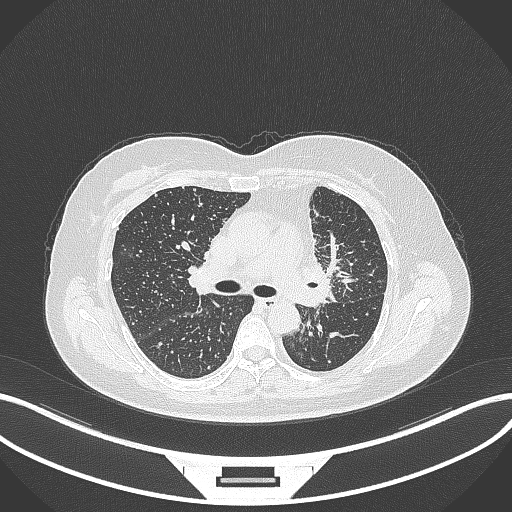
Chest CT, one axial slice; position 207 of 348 along the scan axis; reconstruction kernel B70f; 120 kVp; lung window (W 1500 / L -600 HU); 512 × 512 image matrix, field of view 400 × 400 mm. Female patient, age 49 years. Case-level facts recorded for this patient, not image findings: clinical TNM (as recorded): T1c N0 M1.
Outlined on this slice (rectangle marked by the reading radiologist):
- lung tumour (recorded histology: adenocarcinoma): box from (x=290, y=250) to (x=338, y=312) px